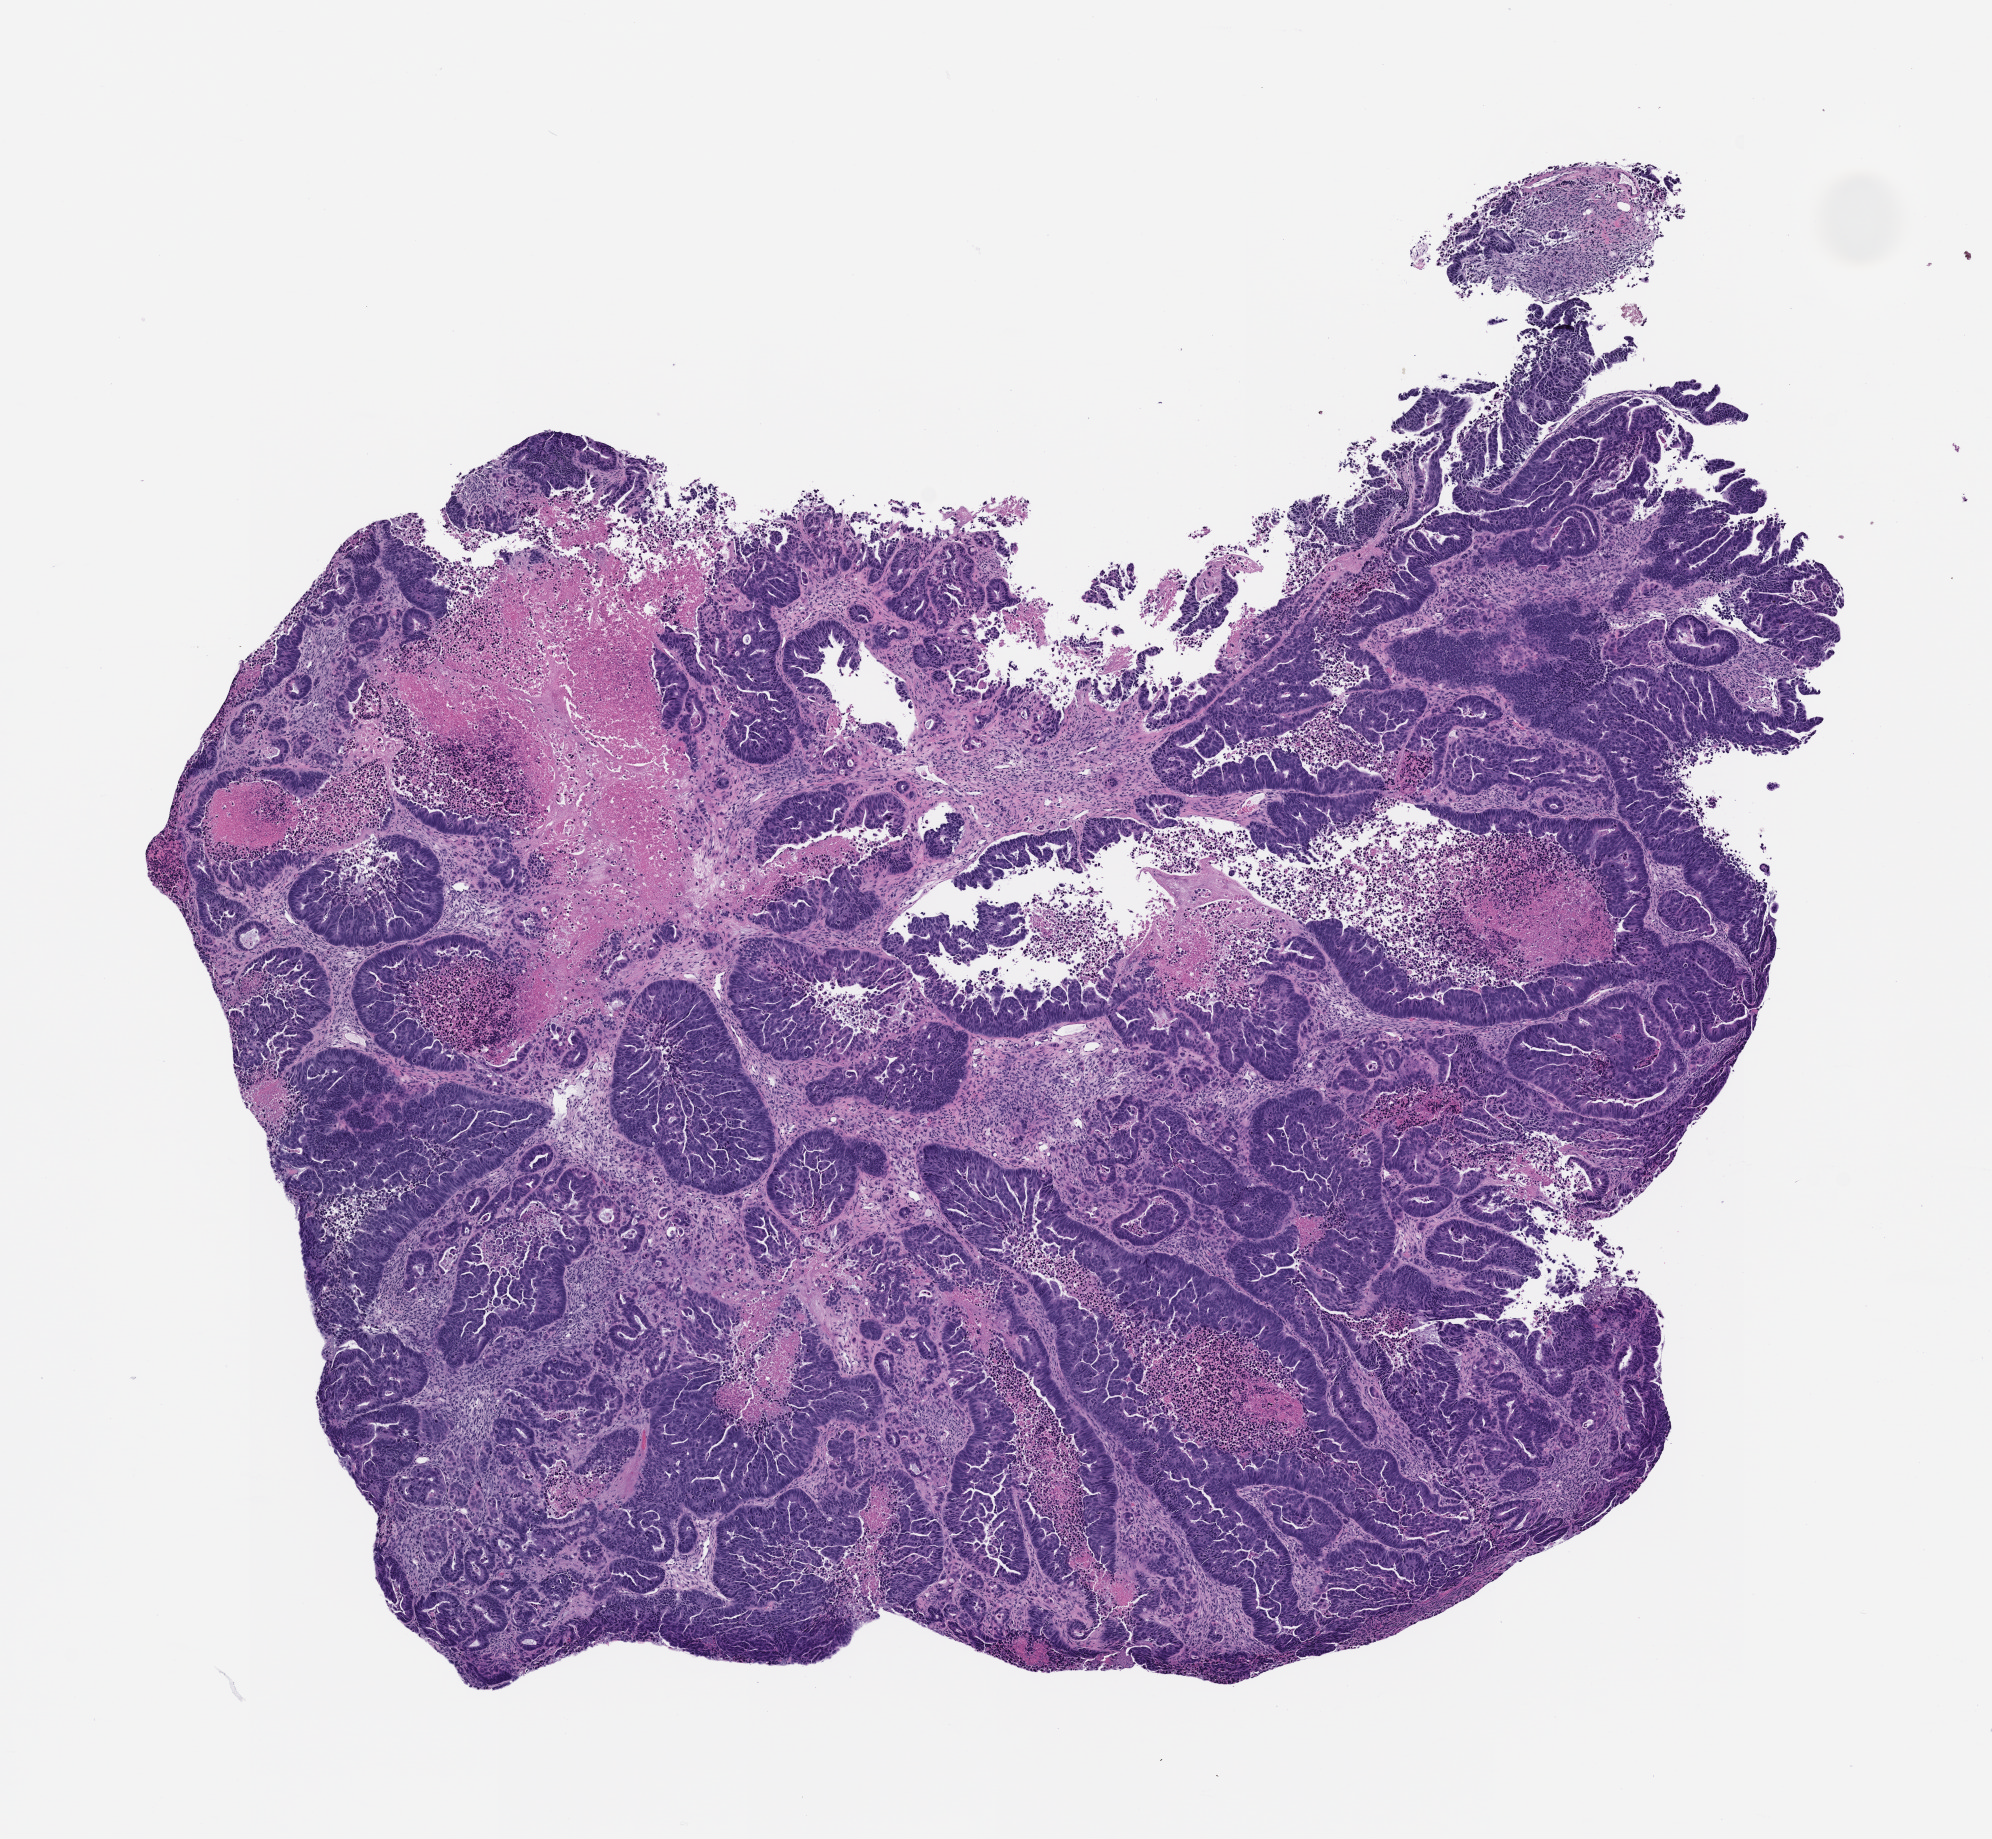
Haematoxylin and eosin whole-slide image of a patient-derived xenograft (PDX) tumor grown in a mouse, passage 1, a low-resolution overview of the entire scanned area, about 8.0 x 7.4 mm. Formalin-fixed, paraffin-embedded (FFPE) tissue. Originating tumor site category: rectum.
* originating patient diagnosis: Rectal Adenocarcinoma